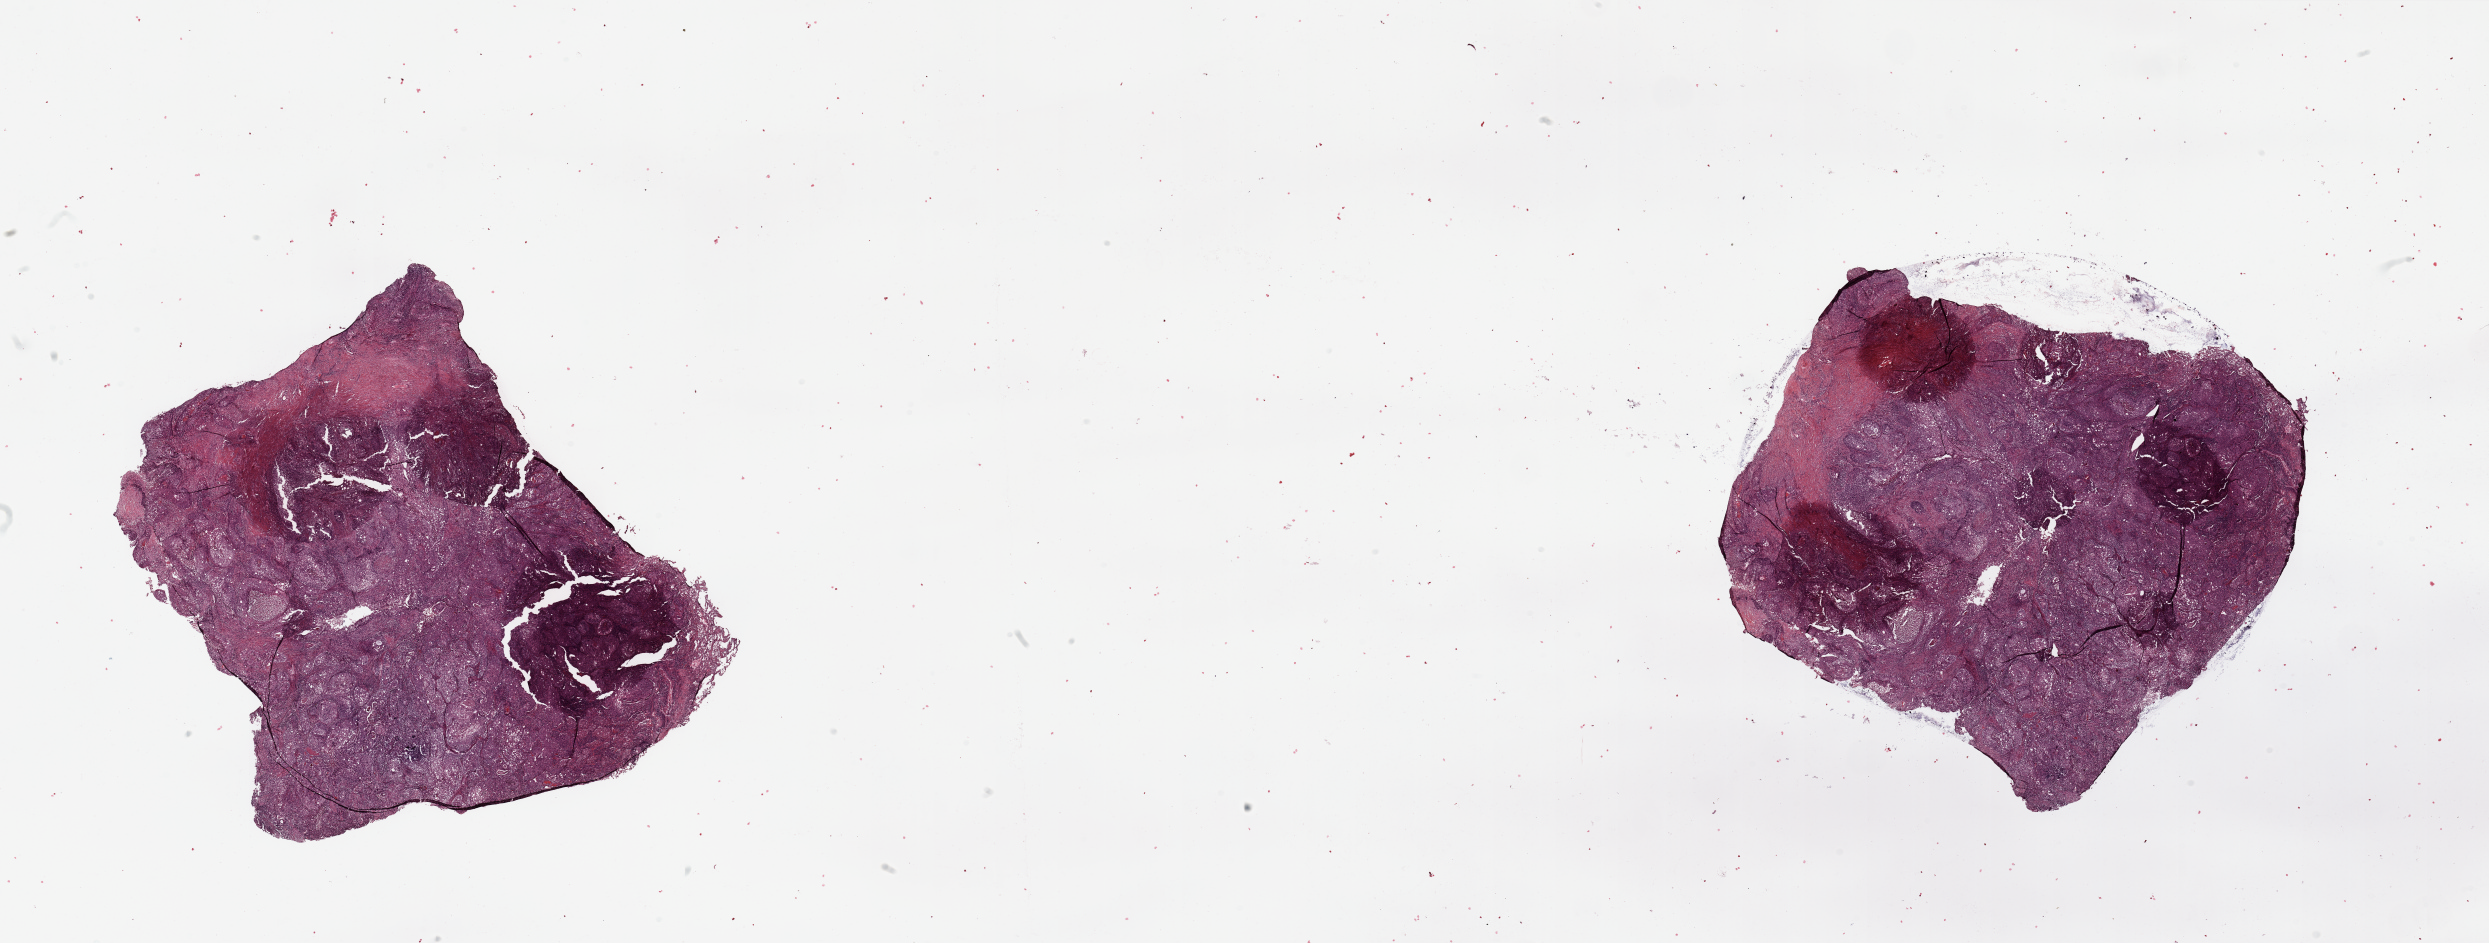
Hematoxylin and eosin (H&E) stained whole-slide image — whole scanned area (about 39.4 x 14.9 mm, slide scanned at 20x) shown as a low-resolution overview, lung, tumour tissue. Patient: male, age 68 years.
• patient diagnosis (cohort enrolment): squamous cell carcinoma (lung)